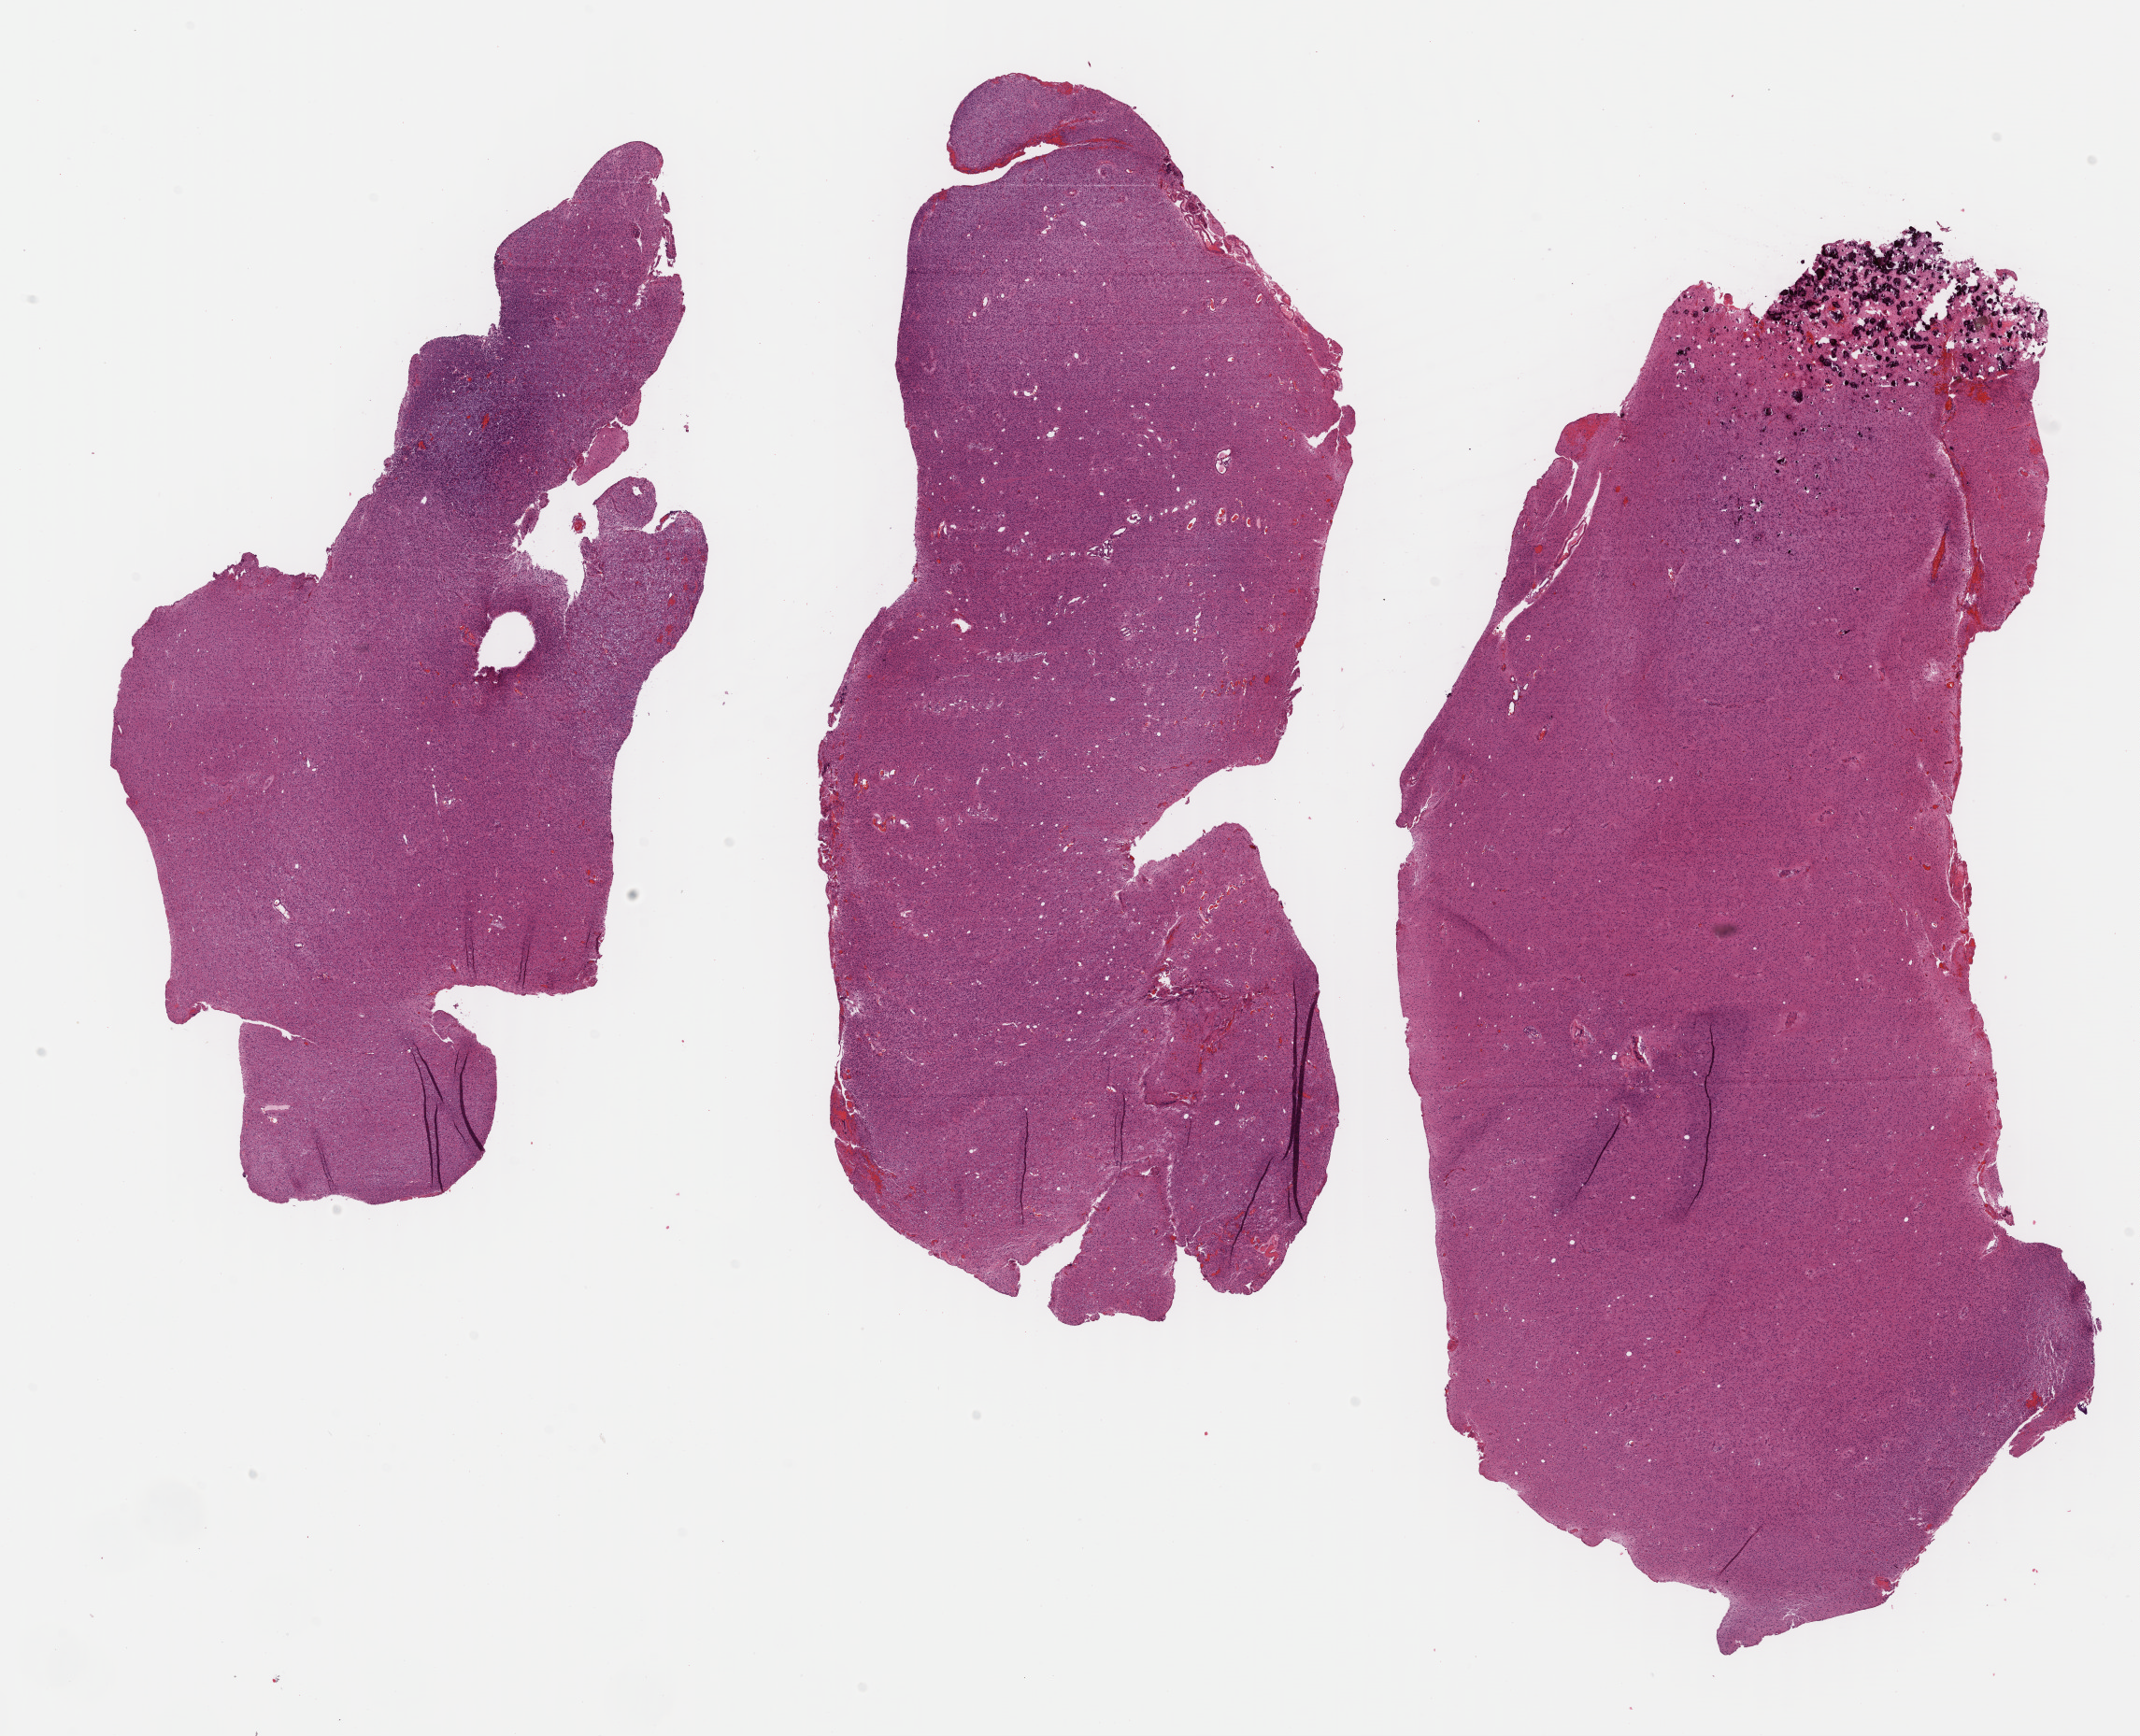
Whole-slide histology image, H&E, a low-resolution overview of the entire scanned area, about 18.0 x 14.6 mm (acquisition: 40x scan), formalin-fixed paraffin-embedded (FFPE) diagnostic section, sample: primary tumour, brain. Patient: male, age at initial diagnosis 30 years. Histologic grade: G3 (poorly differentiated).
Diagnosis: Oligodendroglioma, anaplastic.